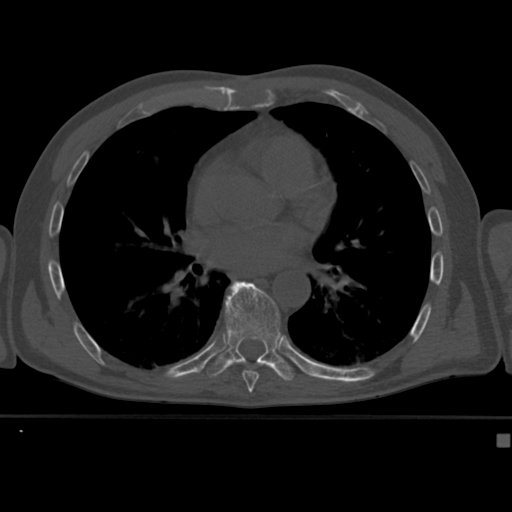
CT including the spine, one axial slice; position 253 of 430 along the scan axis; reconstruction kernel Br40s; bone window (W 1800 / L 400 HU); 1.5 mm slice thickness; 512 × 512 image matrix. Male patient, age 64 years. Case-level facts recorded for this patient, not image findings: primary cancer: uterus; vertebrae with lytic lesions (as recorded): T1, T4, T5, T7, L5.
Outlined on this slice (semi-automatically segmented with operator editing):
- T8 vertebra: bounding box (x1, y1, x2, y2) in pixels: (242, 370, 259, 382)
- T9 vertebra: (206, 281, 296, 382)